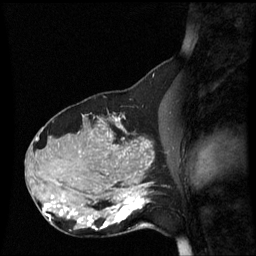
Breast MRI (dynamic contrast-enhanced), one sagittal slice. Slice 27 of 60 in the series (ordered by position). Dynamic contrast-enhanced series, image 2 of 3 at this slice position (ordered by acquisition). 1.5 T. TE 4.2 ms, TR 8.9 ms. 256 × 256 image matrix, field of view 220 × 220 mm. Patient: female, 31 years. Case-level facts recorded for this patient, not image findings: setting: breast cancer imaged before/during neoadjuvant chemotherapy; receptor status: HR-positive, HER2-negative.
Structures marked on this image (semi-automatic segmentation, software-assisted and operator-edited):
- analysis volume of interest (the breast-tissue region the enhancement analysis was run in; not a lesion): bounding box (x1, y1, x2, y2) in pixels: (90, 180, 152, 237)
- tumour enhancement mask (voxels above the 70 % enhancement threshold inside the analysis volume of interest): (90, 184, 149, 231)